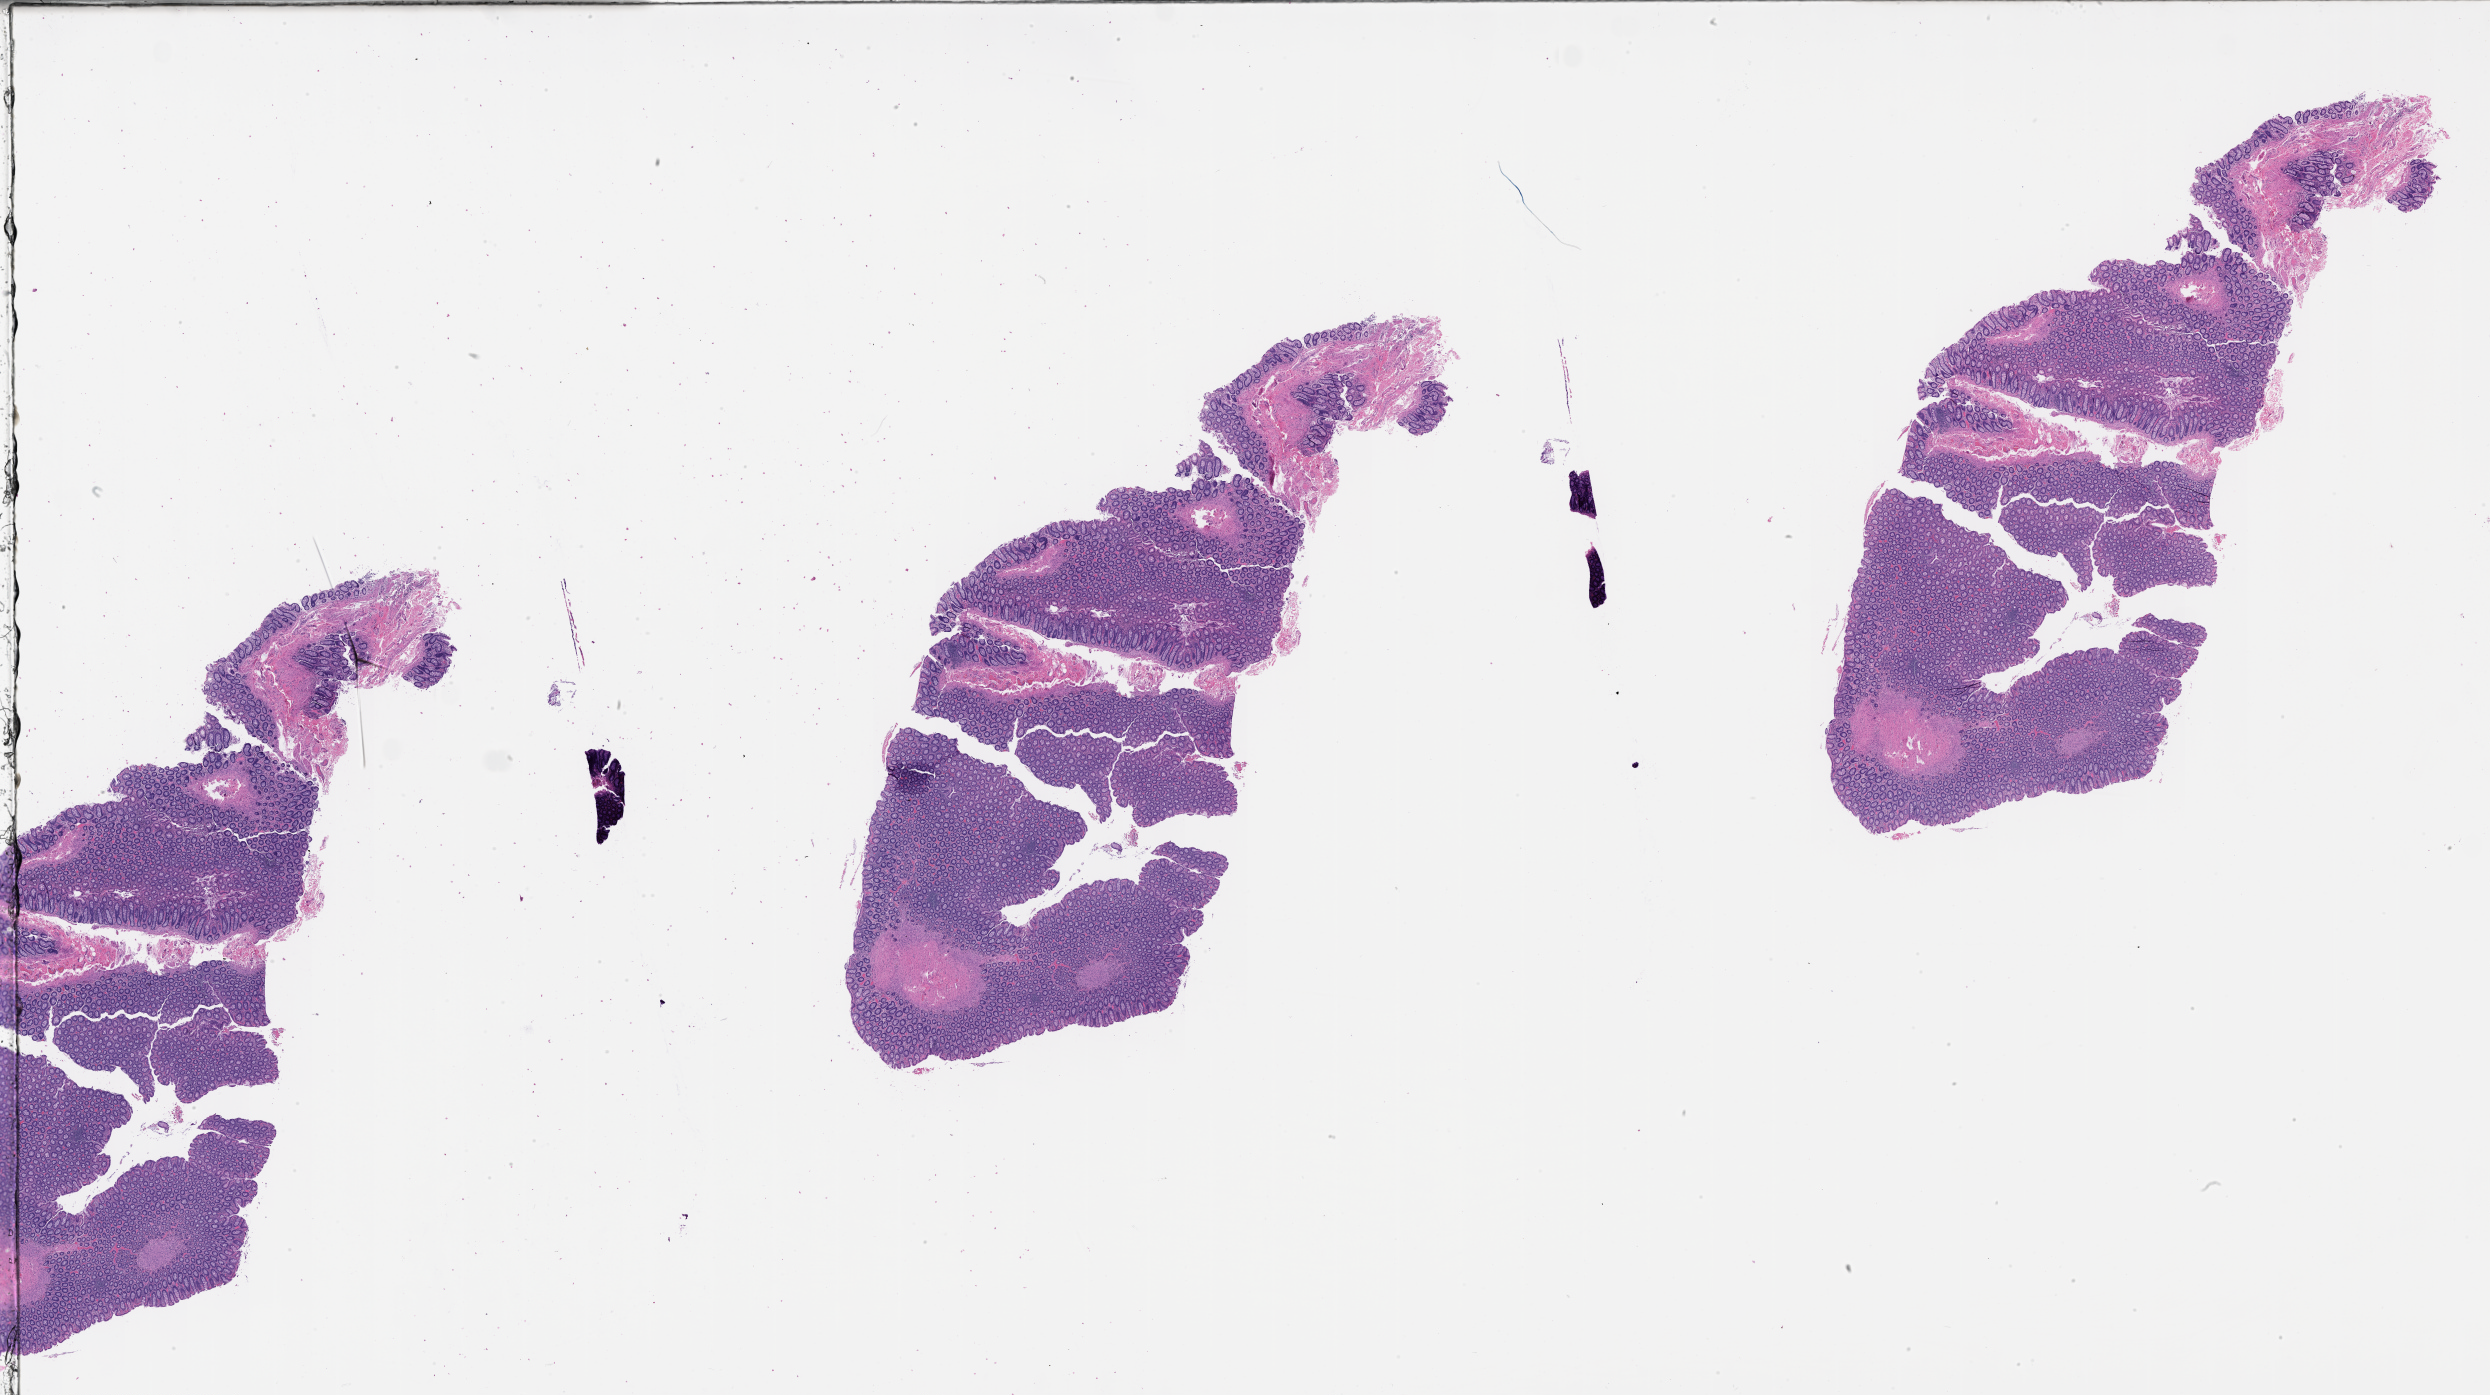
Whole-slide histology image, Hematoxylin and eosin (H&E) stained — low-resolution overview of the scanned area, about 40.1 x 22.5 mm (slide scanned at 20x).
- patient diagnosis (cohort enrolment): sarcoma (site not recorded at cohort level)